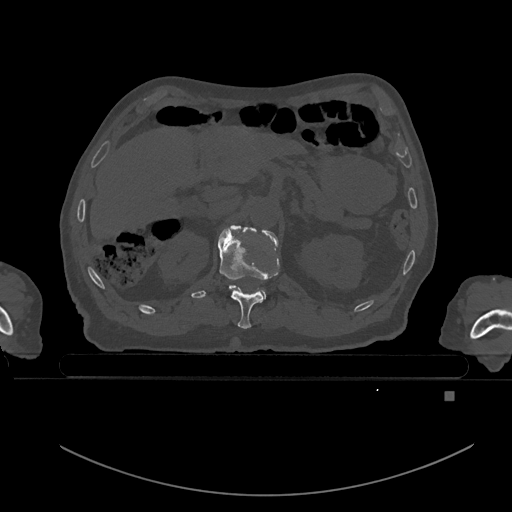
CT including the spine, one axial slice. Slice 6 of 969 in the series (ordered by position). Bone window (W 1800 / L 400 HU). 0.5 mm slice thickness. 512 × 512 image matrix. Patient: male, 82 years. Case-level facts recorded for this patient, not image findings: primary cancer: prostate; vertebrae with lytic lesions (as recorded): T11, T9, T8, T2.
Outlined on this slice (semi-automatic segmentation, software-assisted and operator-edited):
- T11 vertebra: bounding box [x1, y1, x2, y2] px = [218, 227, 279, 329]